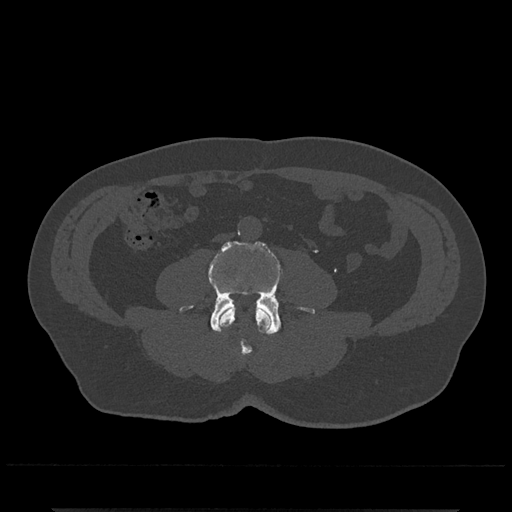
CT including the spine, one axial slice. Position 176 of 797 along the scan axis. Bone window (W 1800 / L 400 HU). 0.5 mm slice thickness. 512 × 512 image matrix. Male patient, age 67 years. Case-level facts recorded for this patient, not image findings: primary cancer: prostate.
Outlined on this slice (semi-automatically segmented with operator editing):
- L3 vertebra: bounding box <219,307,272,356> (left, top, right, bottom; pixels)
- L4 vertebra: <179,241,315,335>